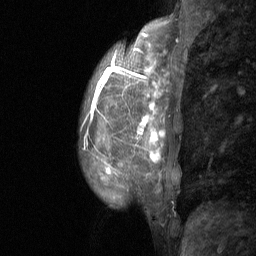
Breast MRI (dynamic contrast-enhanced), one sagittal slice. Position 19 of 64 along the scan axis. Dynamic contrast-enhanced study with each time point stored as its own series, time point 2 of 3 at this slice position (early post-contrast, ordered by acquisition time). 1.5 T. TE 4.8 ms, TR 27 ms. 2 mm slice thickness. 256 × 256 image matrix, field of view 180 × 180 mm. Female patient, age 36 years. Case-level facts recorded for this patient, not image findings: setting: breast cancer imaged before/during neoadjuvant chemotherapy; receptor status: HR-positive, HER2-negative.
Structures marked on this image (semi-automatically segmented with operator editing):
- analysis volume of interest (the breast-tissue region the enhancement analysis was run in; not a lesion): bounding box (x1, y1, x2, y2) in pixels: (79, 12, 214, 233)
- tumour enhancement mask (voxels above the 90 % enhancement threshold inside the analysis volume of interest): (144, 35, 167, 162)